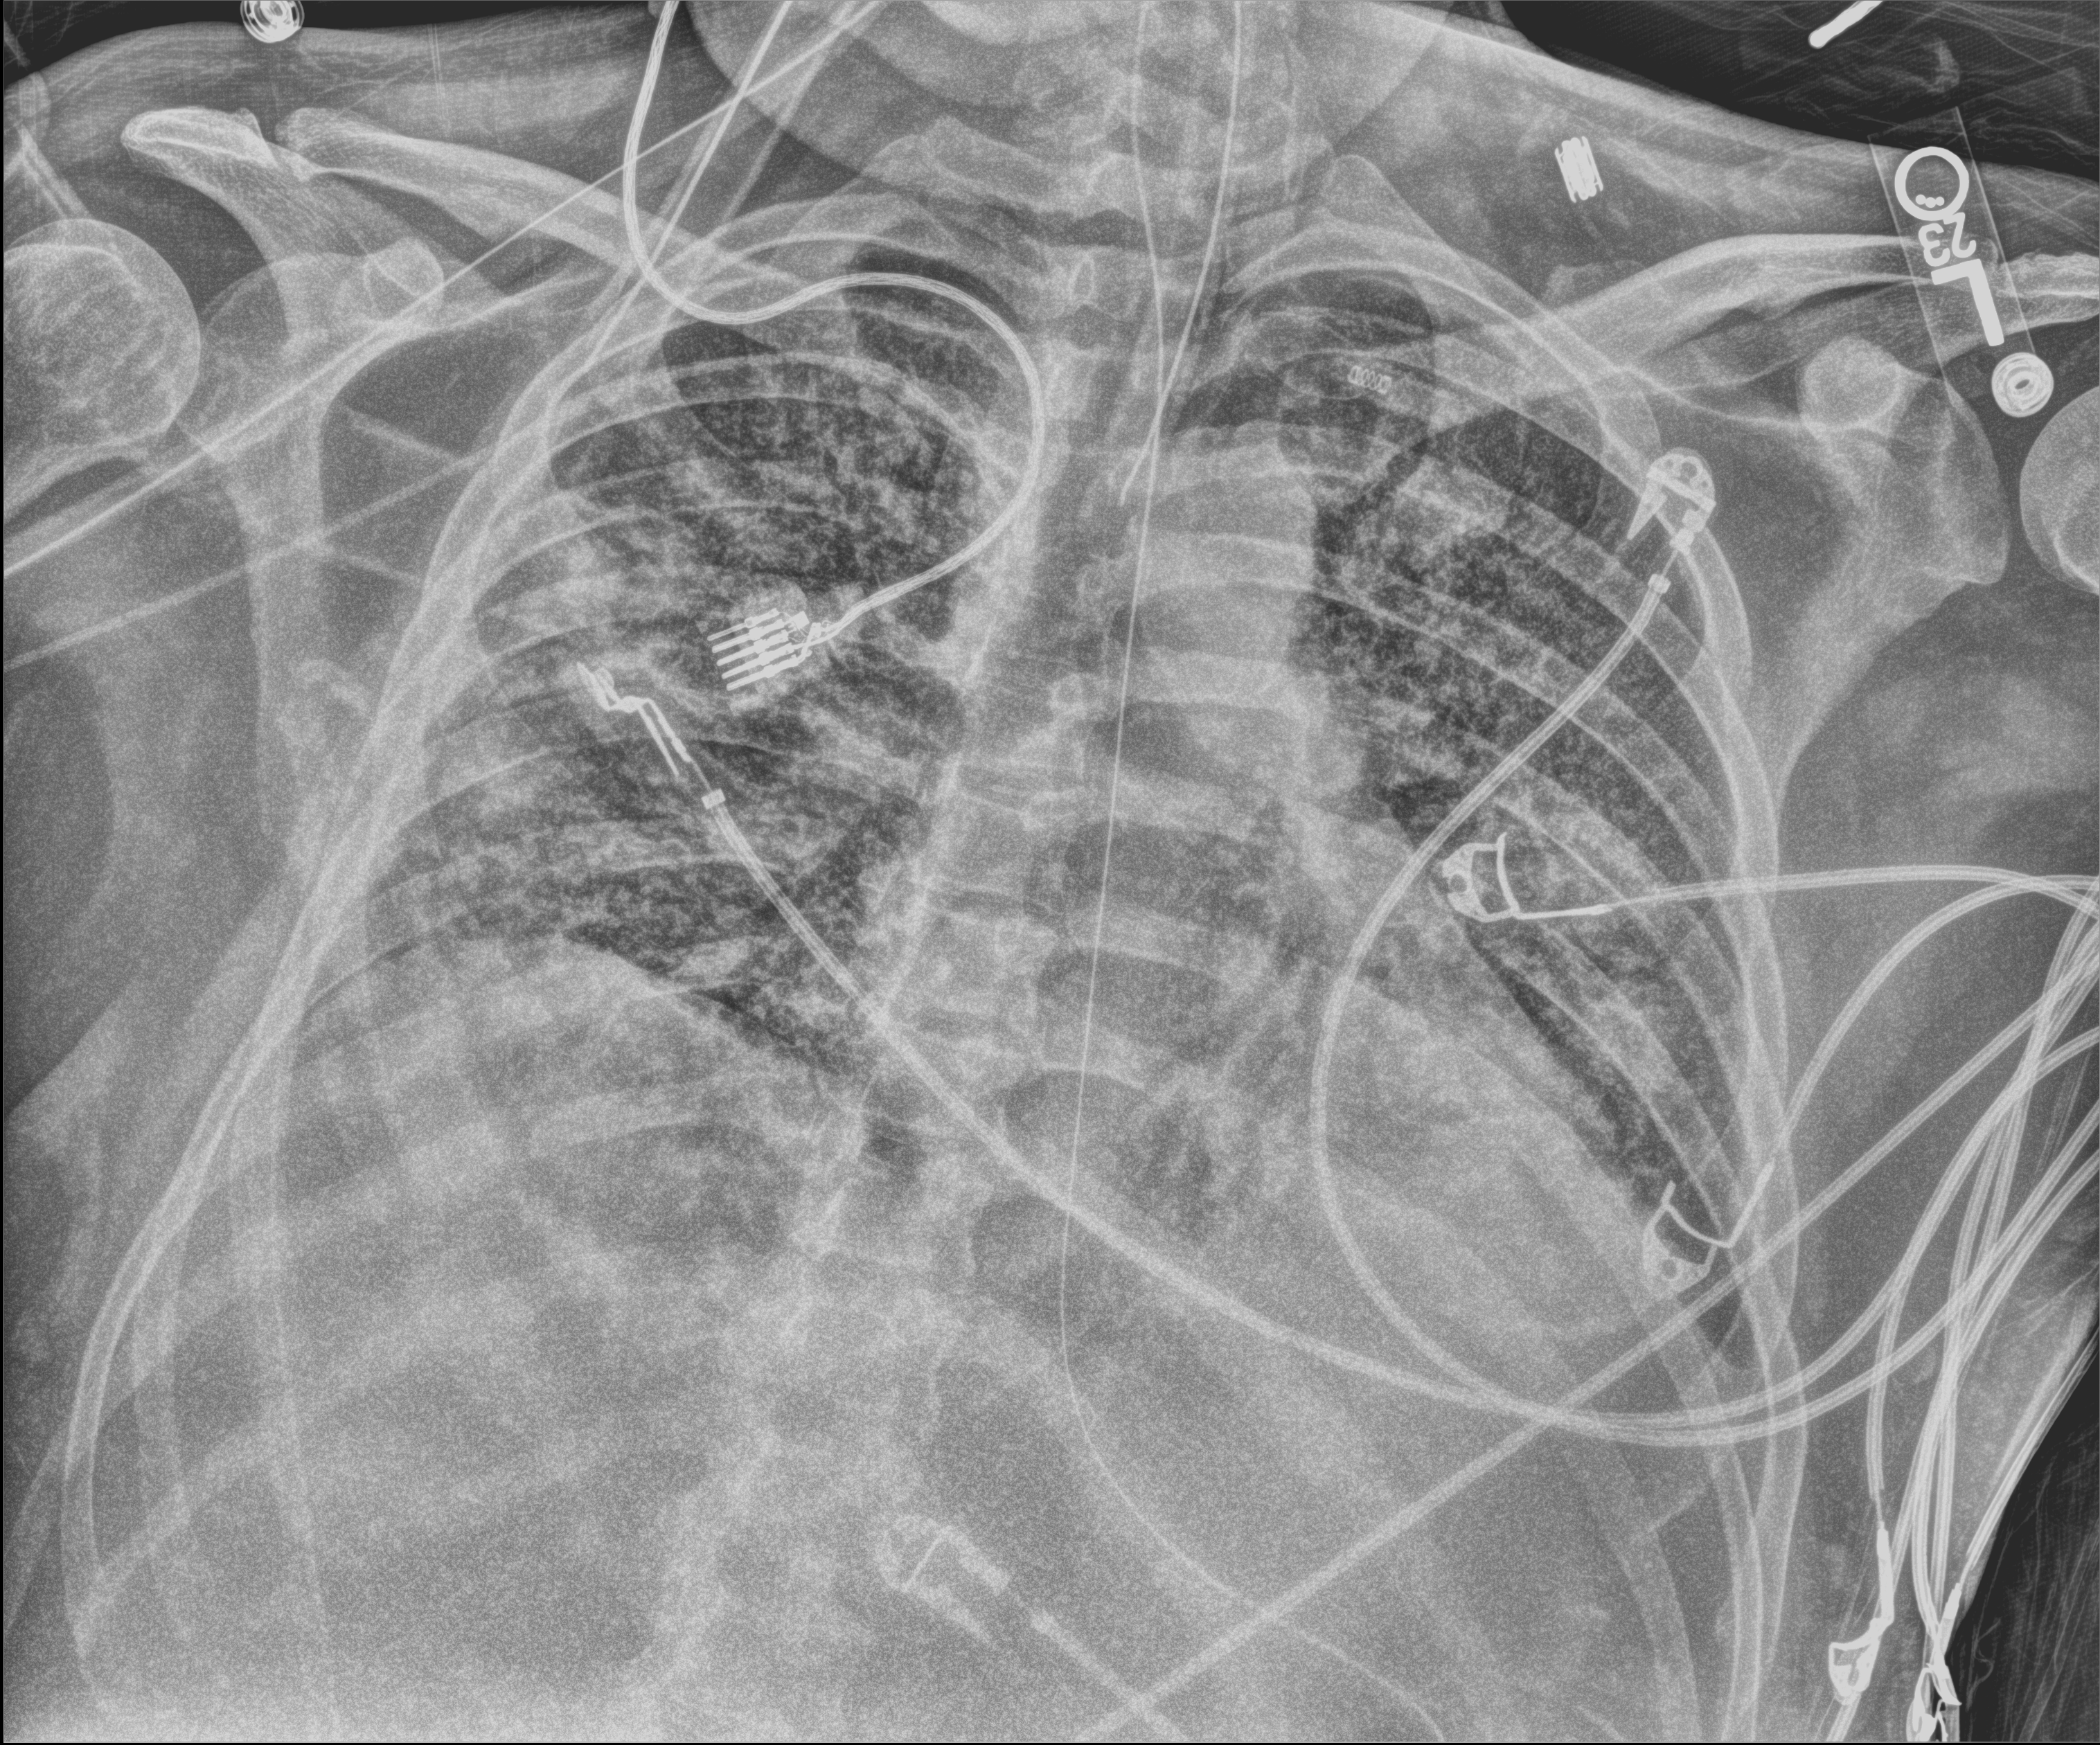
Portable chest radiograph; anteroposterior (AP) projection. Male patient hospitalised with COVID-19, age 18–59 years.
From the hospital-stay record, not from the radiograph (when in the stay this image was taken is not recorded): other chronic lung disease (admission record): no; diabetes (admission record): no.